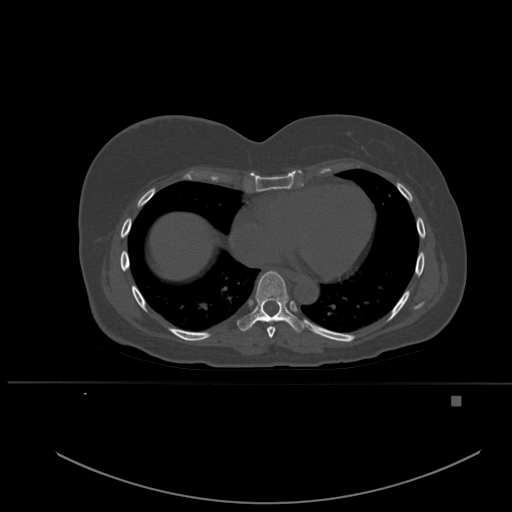
CT including the spine, one axial slice. Position 324 of 651 along the scan axis. Bone window (W 1800 / L 400 HU). 512 × 512 image matrix. Patient: female, 49 years. From the clinical record (not read from this slice): primary cancer: breast.
Annotated regions visible in this slice (semi-automatic segmentation, software-assisted and operator-edited):
- T7 vertebra: bounding box <267,326,276,338> (left, top, right, bottom; pixels)
- T8 vertebra: <237,271,305,333>